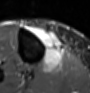
MRI of an extremity soft-tissue mass, one axial slice. Position 28 of 60 along the scan axis. STIR. MR volume resampled by the dataset authors to the PET/CT grid (not the native acquisition matrix). 3.27 mm slice thickness. 90 × 93 image matrix, field of view 88 × 91 mm. Female patient. Case-level facts recorded for this patient, not image findings: histological type: undifferentiated – high grade; grade: high; site of the primary tumour: right thigh.
Annotated regions visible in this slice (expert contour drawn on MRI and transferred to this co-registered scan by the dataset authors):
- gross tumour volume (mass): bounding box [x1, y1, x2, y2] px = [33, 28, 63, 72]